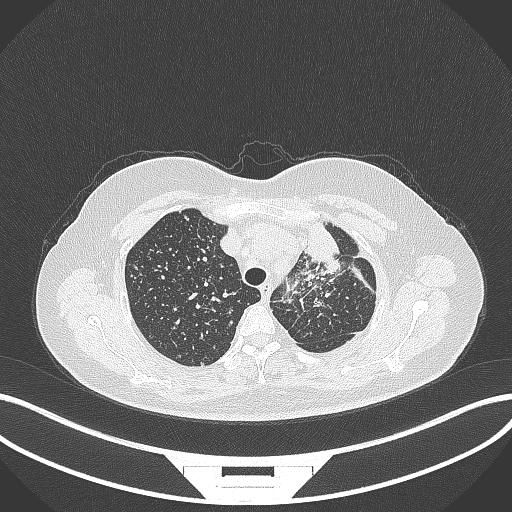
Chest CT, one axial slice. Position 265 of 348 along the scan axis. 120 kVp. Lung window (W 1500 / L -600 HU). 1 mm slice thickness. 512 × 512 image matrix. Patient: female, 49 years. Case-level facts recorded for this patient, not image findings: clinical TNM (as recorded): T1c N0 M1.
Structures marked on this image (bounding box drawn by a radiologist):
- lung tumour (recorded histology: adenocarcinoma): bounding box [x1, y1, x2, y2] px = [298, 220, 344, 271]